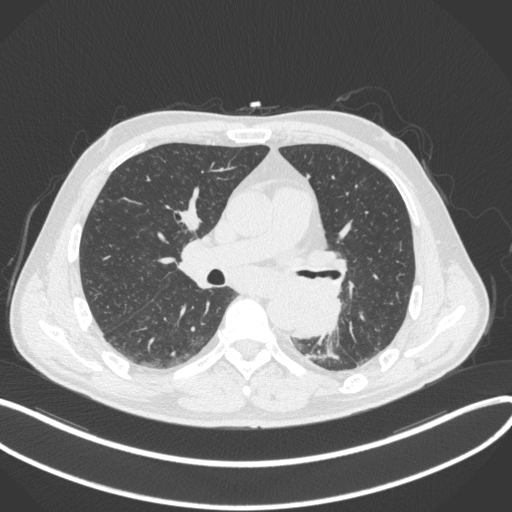
Chest CT, one axial slice. Position 187 of 328 along the scan axis. Lung window (W 1500 / L -600 HU). 1 mm slice thickness. 512 × 512 image matrix, field of view 400 × 400 mm. Male patient, age 59 years. Case-level facts recorded for this patient, not image findings: clinical TNM (as recorded): T2a N2 M0.
Outlined on this slice (rectangle marked by the reading radiologist):
- lung tumour (recorded histology: squamous cell carcinoma): box from (x=287, y=281) to (x=342, y=342) px